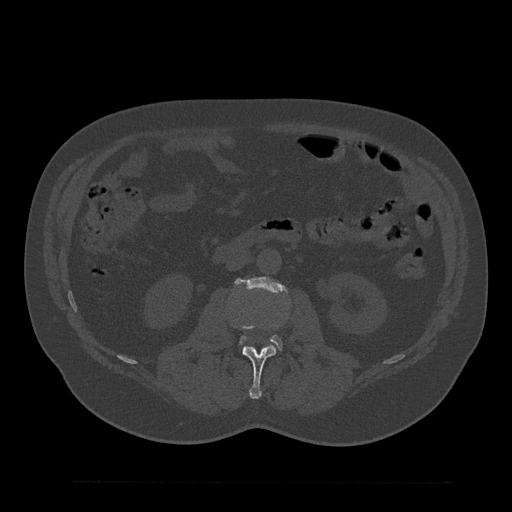
CT including the spine, one axial slice. Slice 74 of 797 in the series (ordered by position). Reconstruction kernel Br40s/3. Bone window (W 1800 / L 400 HU). 512 × 512 image matrix, field of view 430 × 430 mm. Patient: male, 61 years. From the clinical record (not read from this slice): primary cancer: prostate.
Outlined on this slice (semi-automatically segmented with operator editing):
- L2 vertebra: bounding box [x1, y1, x2, y2] px = [230, 320, 276, 399]
- L3 vertebra: [235, 277, 285, 349]